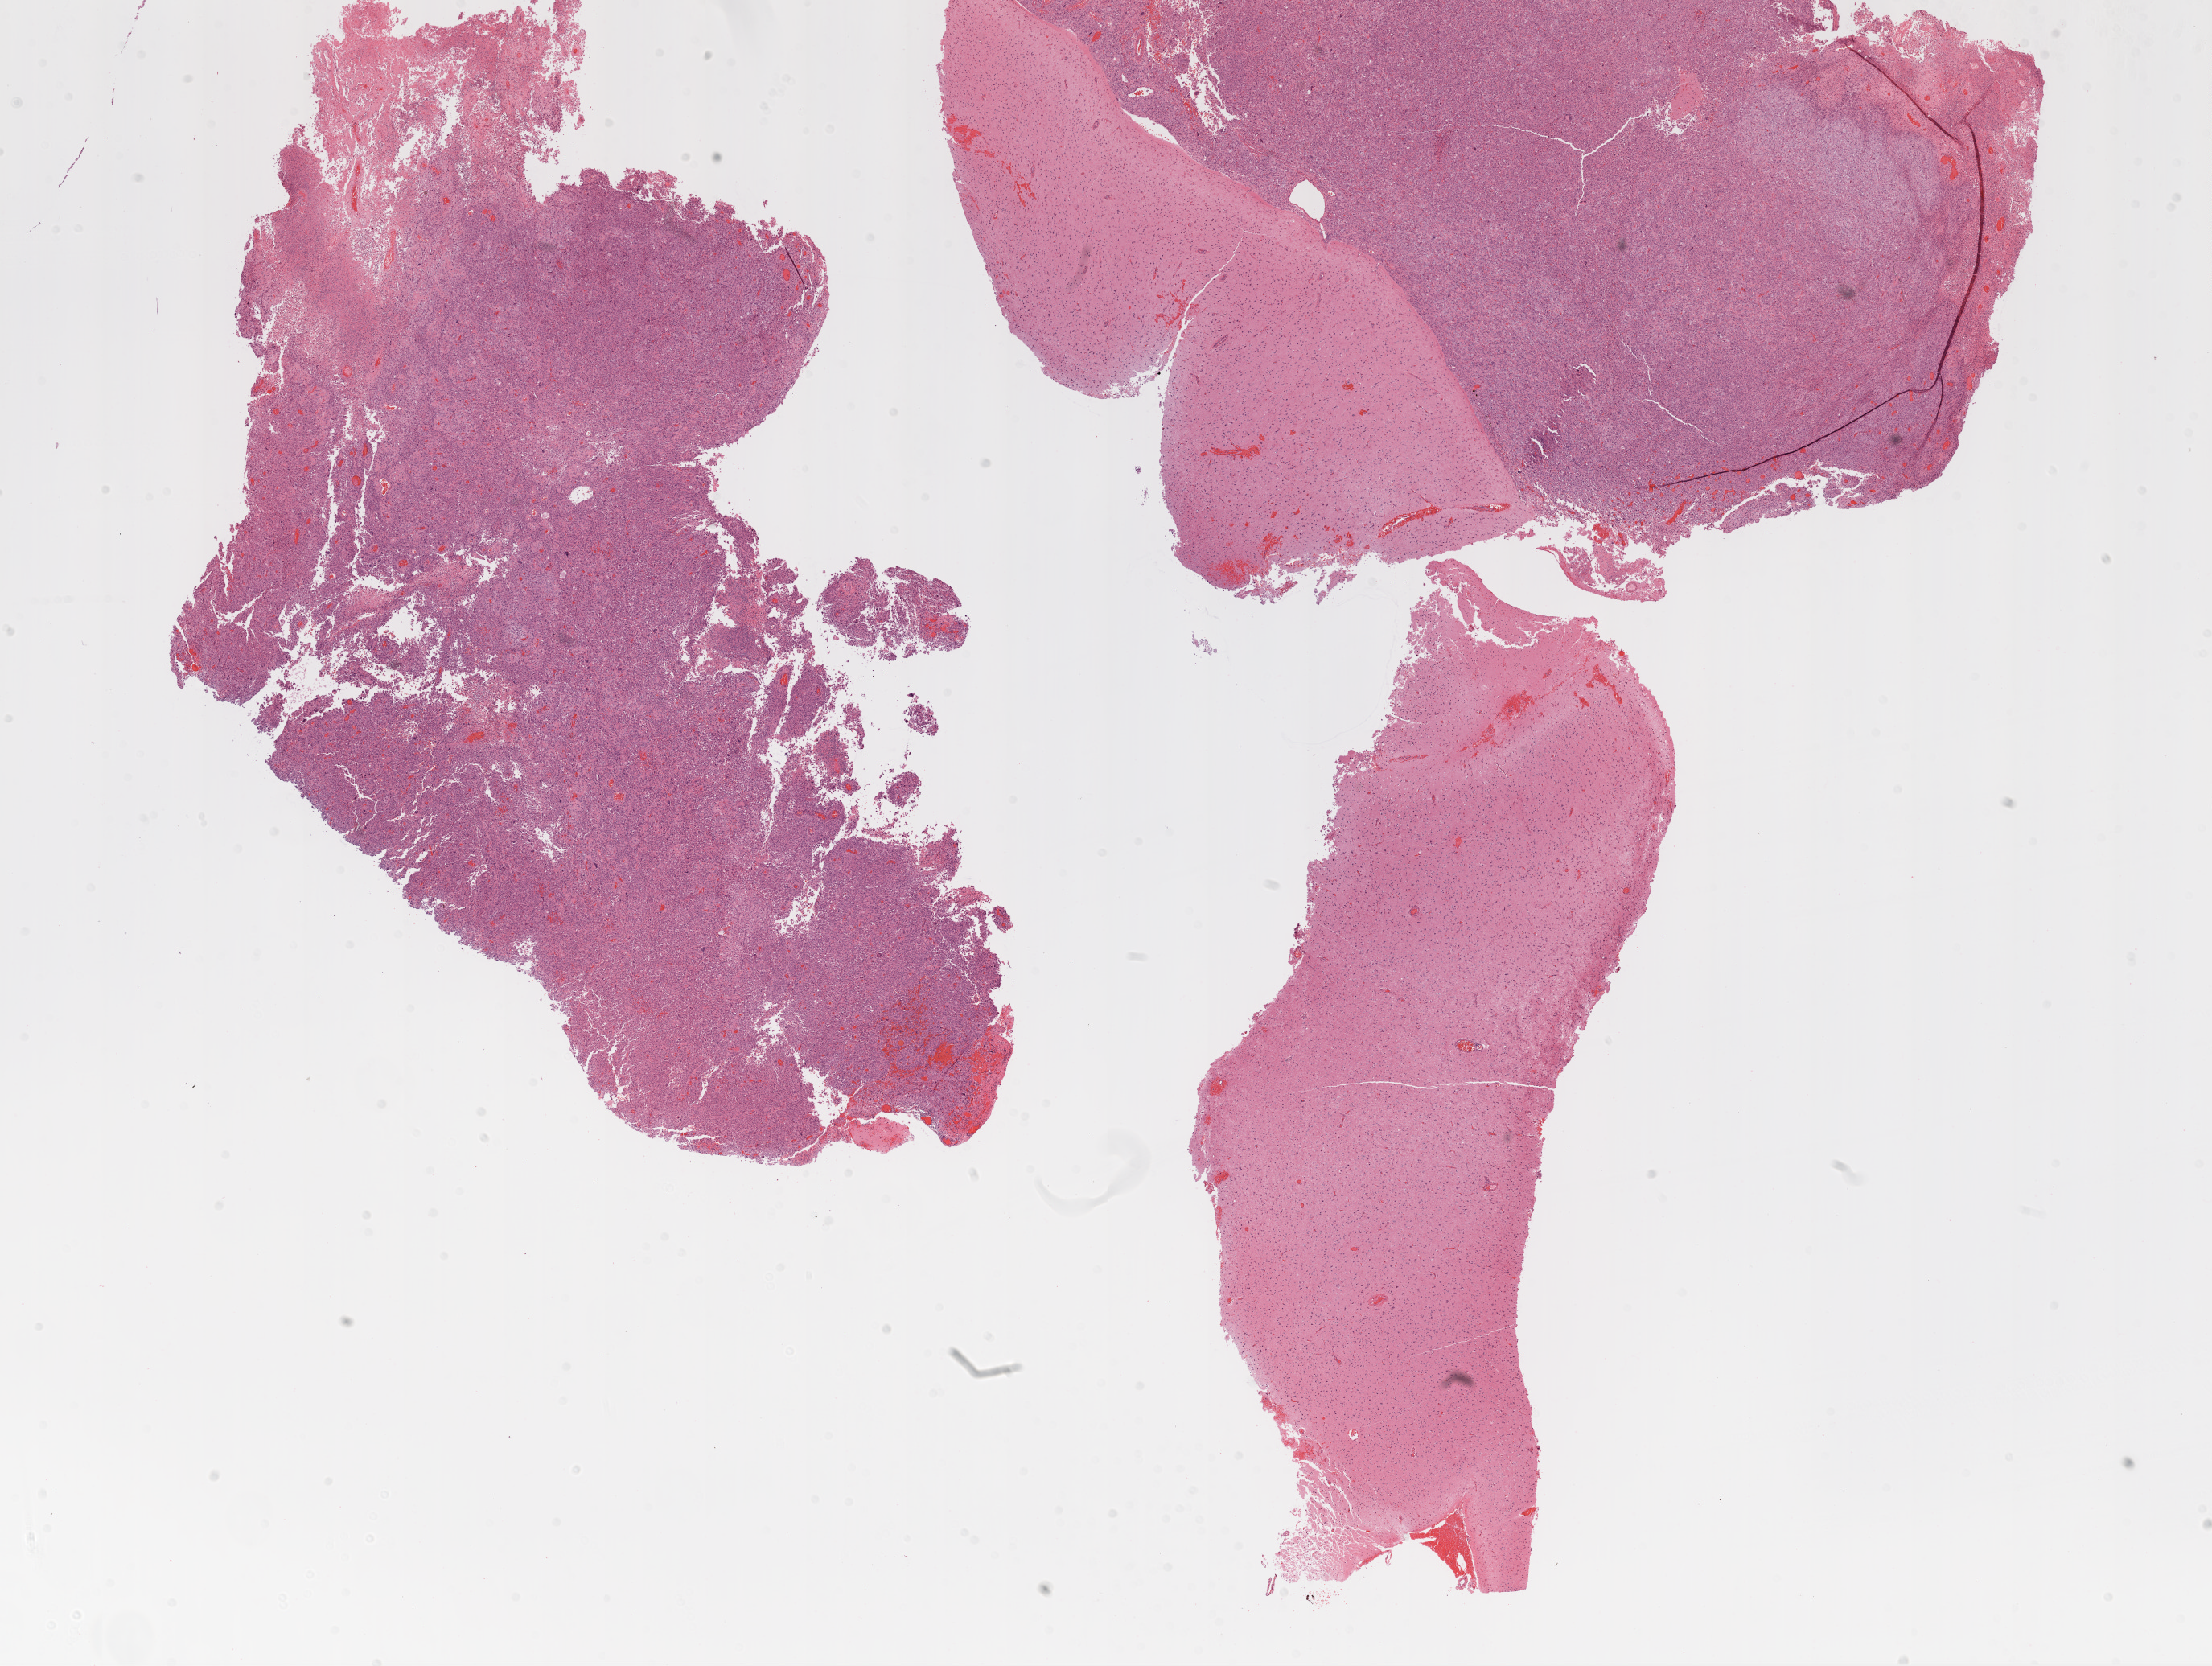
Digitized H&E tissue section (whole slide) — a low-resolution overview of the entire scanned area, about 22.1 x 16.6 mm (acquisition: 20x scan); formalin-fixed paraffin-embedded (FFPE) diagnostic section; brain, primary tumour sample. Male, age 34 years at initial diagnosis.
Diagnosis: Glioblastoma.